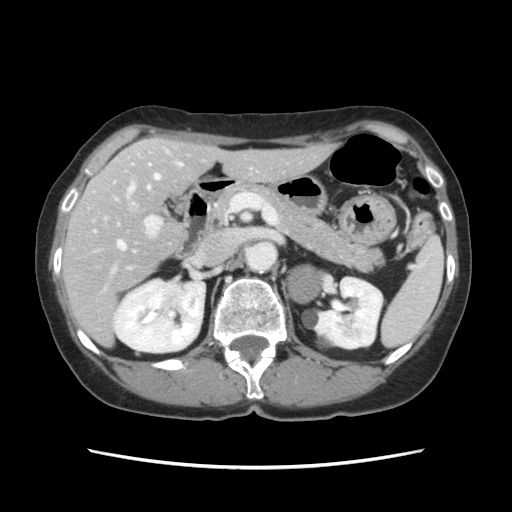
Contrast-enhanced abdominal CT, one axial slice; position 68 of 120 along the scan axis; 120 kVp; intravenous contrast given; soft-tissue window (W 400 / L 40 HU); 2.5 mm slice thickness; 512 × 512 image matrix, field of view 330 × 330 mm. Female patient, age 70 years. From the clinical record (not read from this slice): diagnosis: colorectal cancer liver metastases, imaged before liver resection; multiple liver metastases: no; largest metastasis: 2.5 cm; chemotherapy before resection: yes.
Outlined on this slice (manually delineated by an expert):
- hepatic veins: bounding box (x1, y1, x2, y2) in pixels: (94, 164, 160, 250)
- liver: (64, 139, 331, 344)
- planned liver remnant (the part of the liver to remain after resection): (84, 139, 331, 278)
- portal vein (with intrahepatic branches): (104, 150, 183, 269)